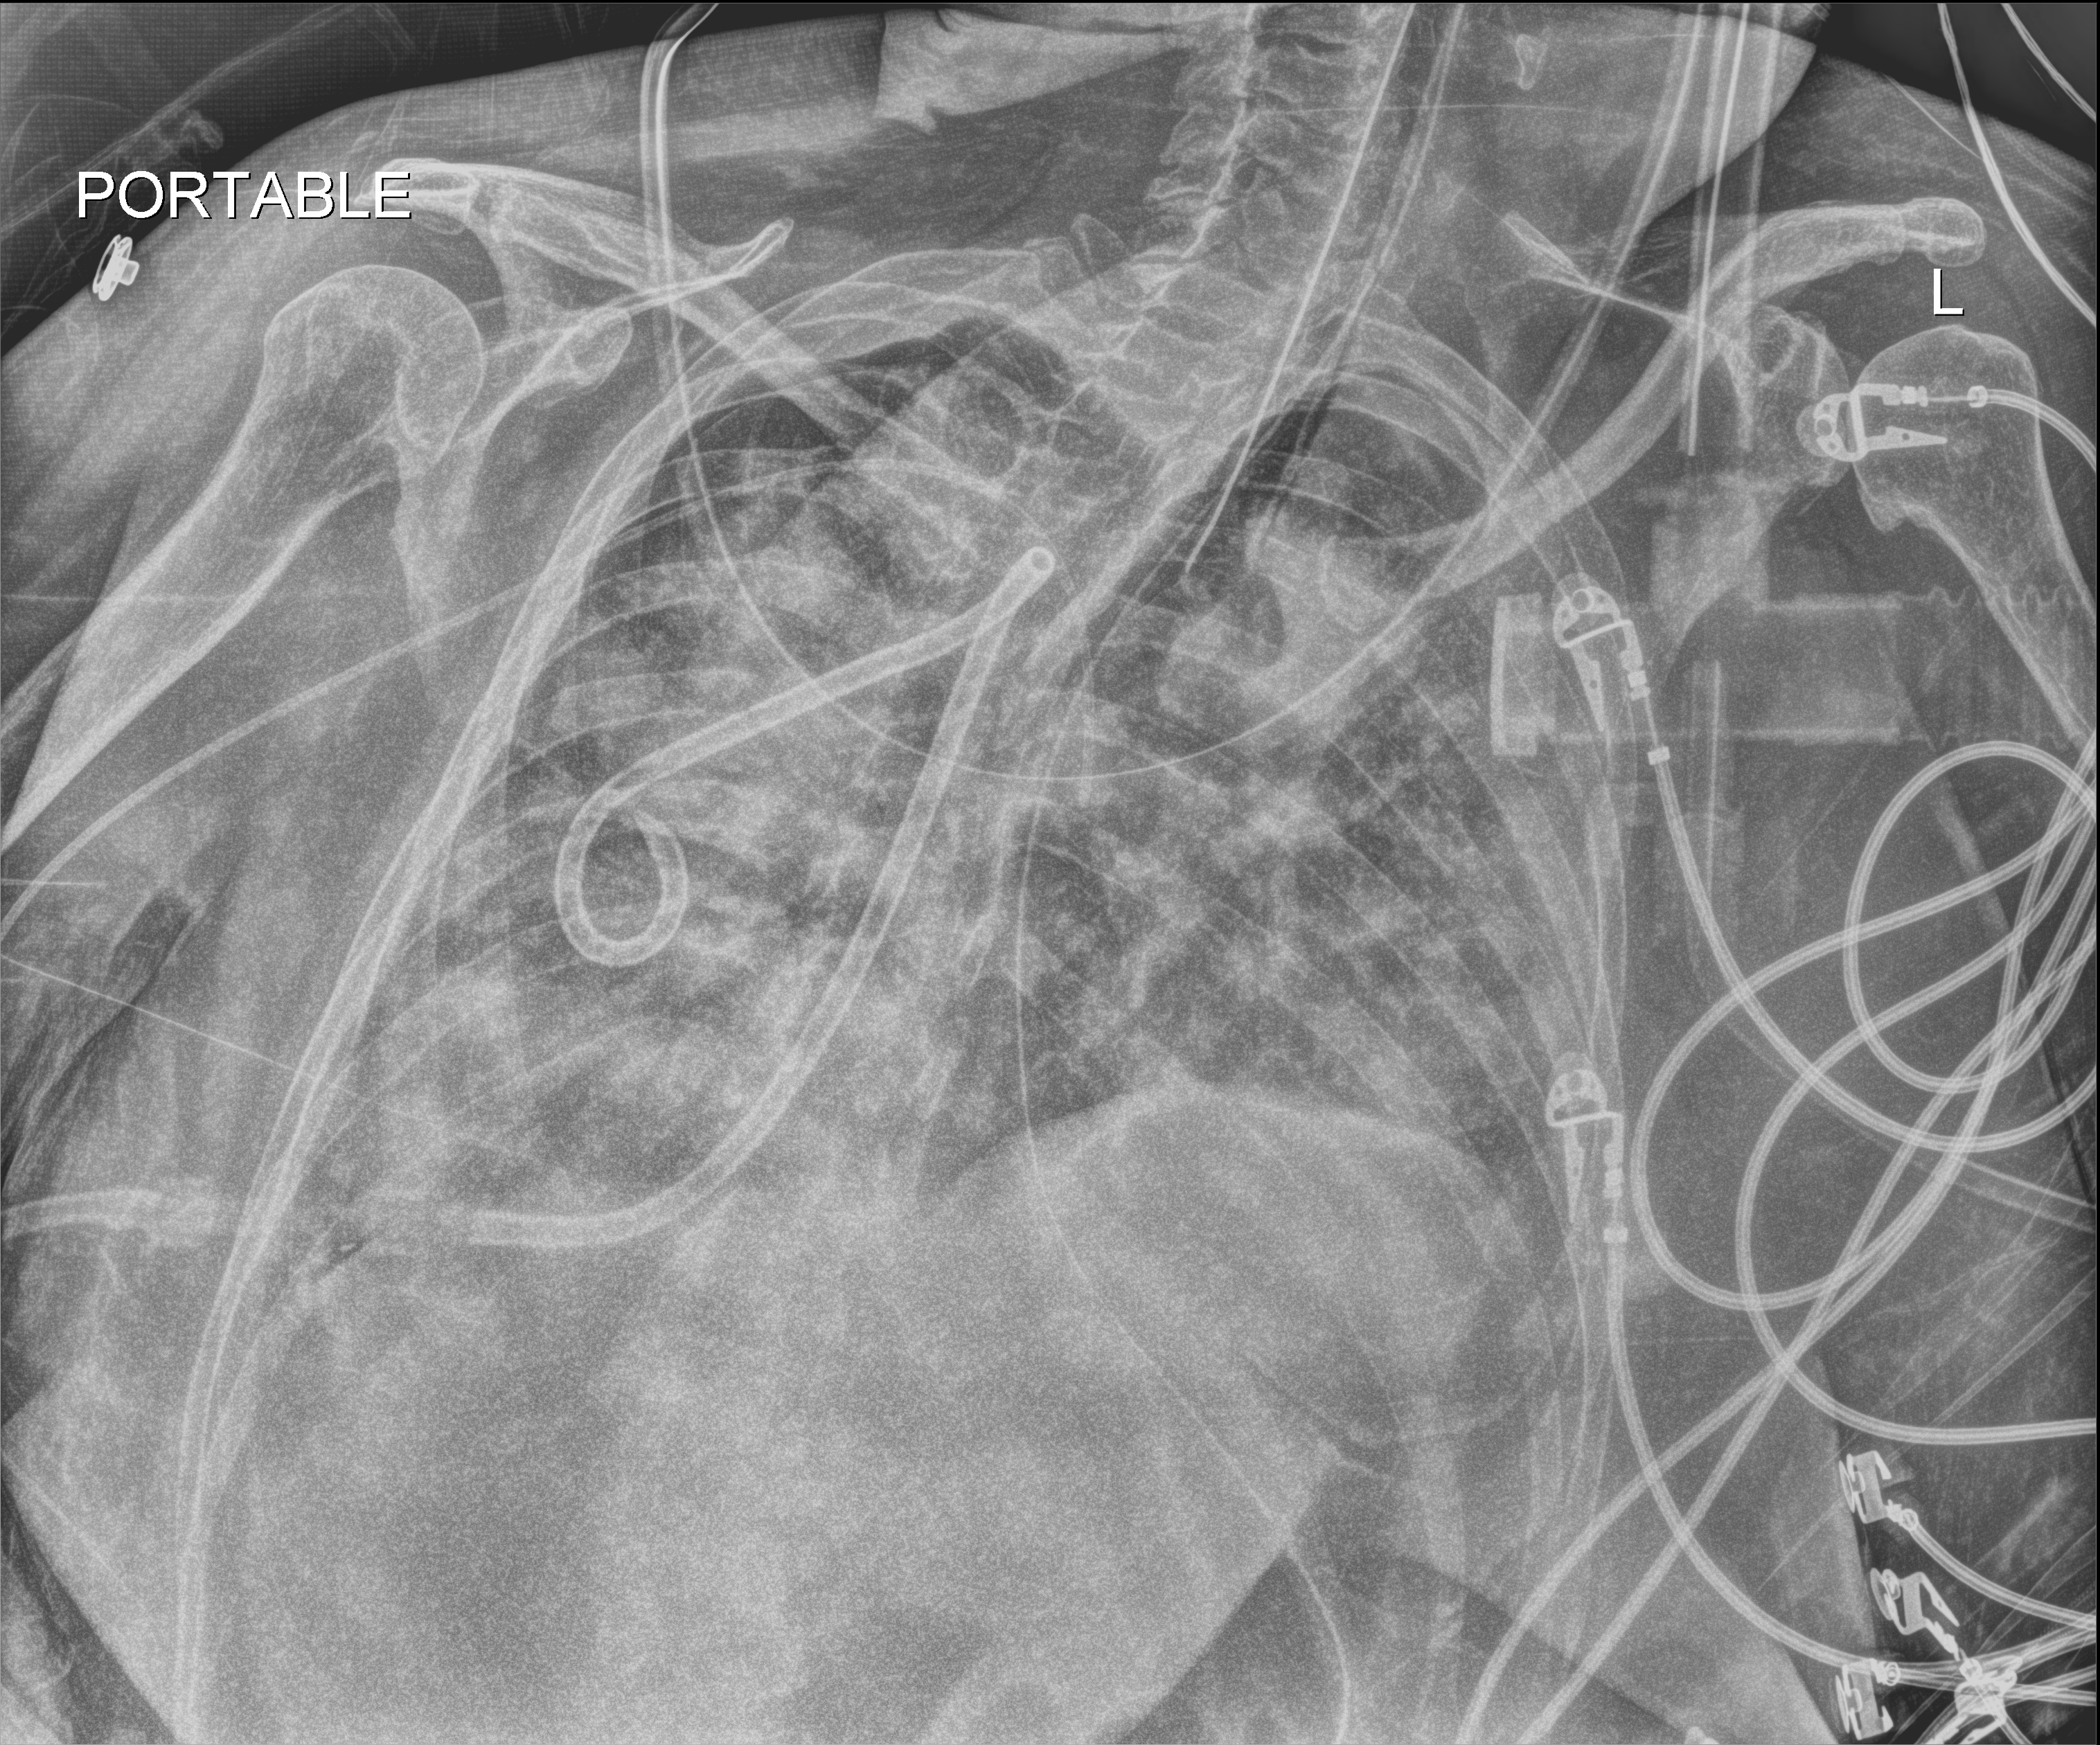
Chest radiograph; anteroposterior (AP) projection. Patient hospitalised with COVID-19, aged 18–59 years.
From the hospital-stay record, not from the radiograph (when in the stay this image was taken is not recorded):
- admitted to intensive care during this hospital stay: yes